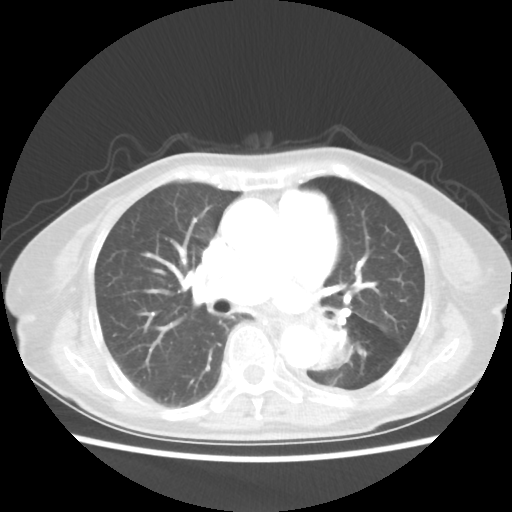
Chest CT, one axial slice. Position 26 of 50 along the scan axis. Reconstruction kernel STANDARD. Lung window (W 1500 / L -600 HU). 5 mm slice thickness. 512 × 512 image matrix. Patient: female, 81 years. Case-level facts recorded for this patient, not image findings: clinical TNM (as recorded): T2 N0 M1a.
Structures marked on this image (rectangle marked by the reading radiologist):
- lung tumour (recorded histology: squamous cell carcinoma): bounding box [x1, y1, x2, y2] px = [309, 319, 358, 377]